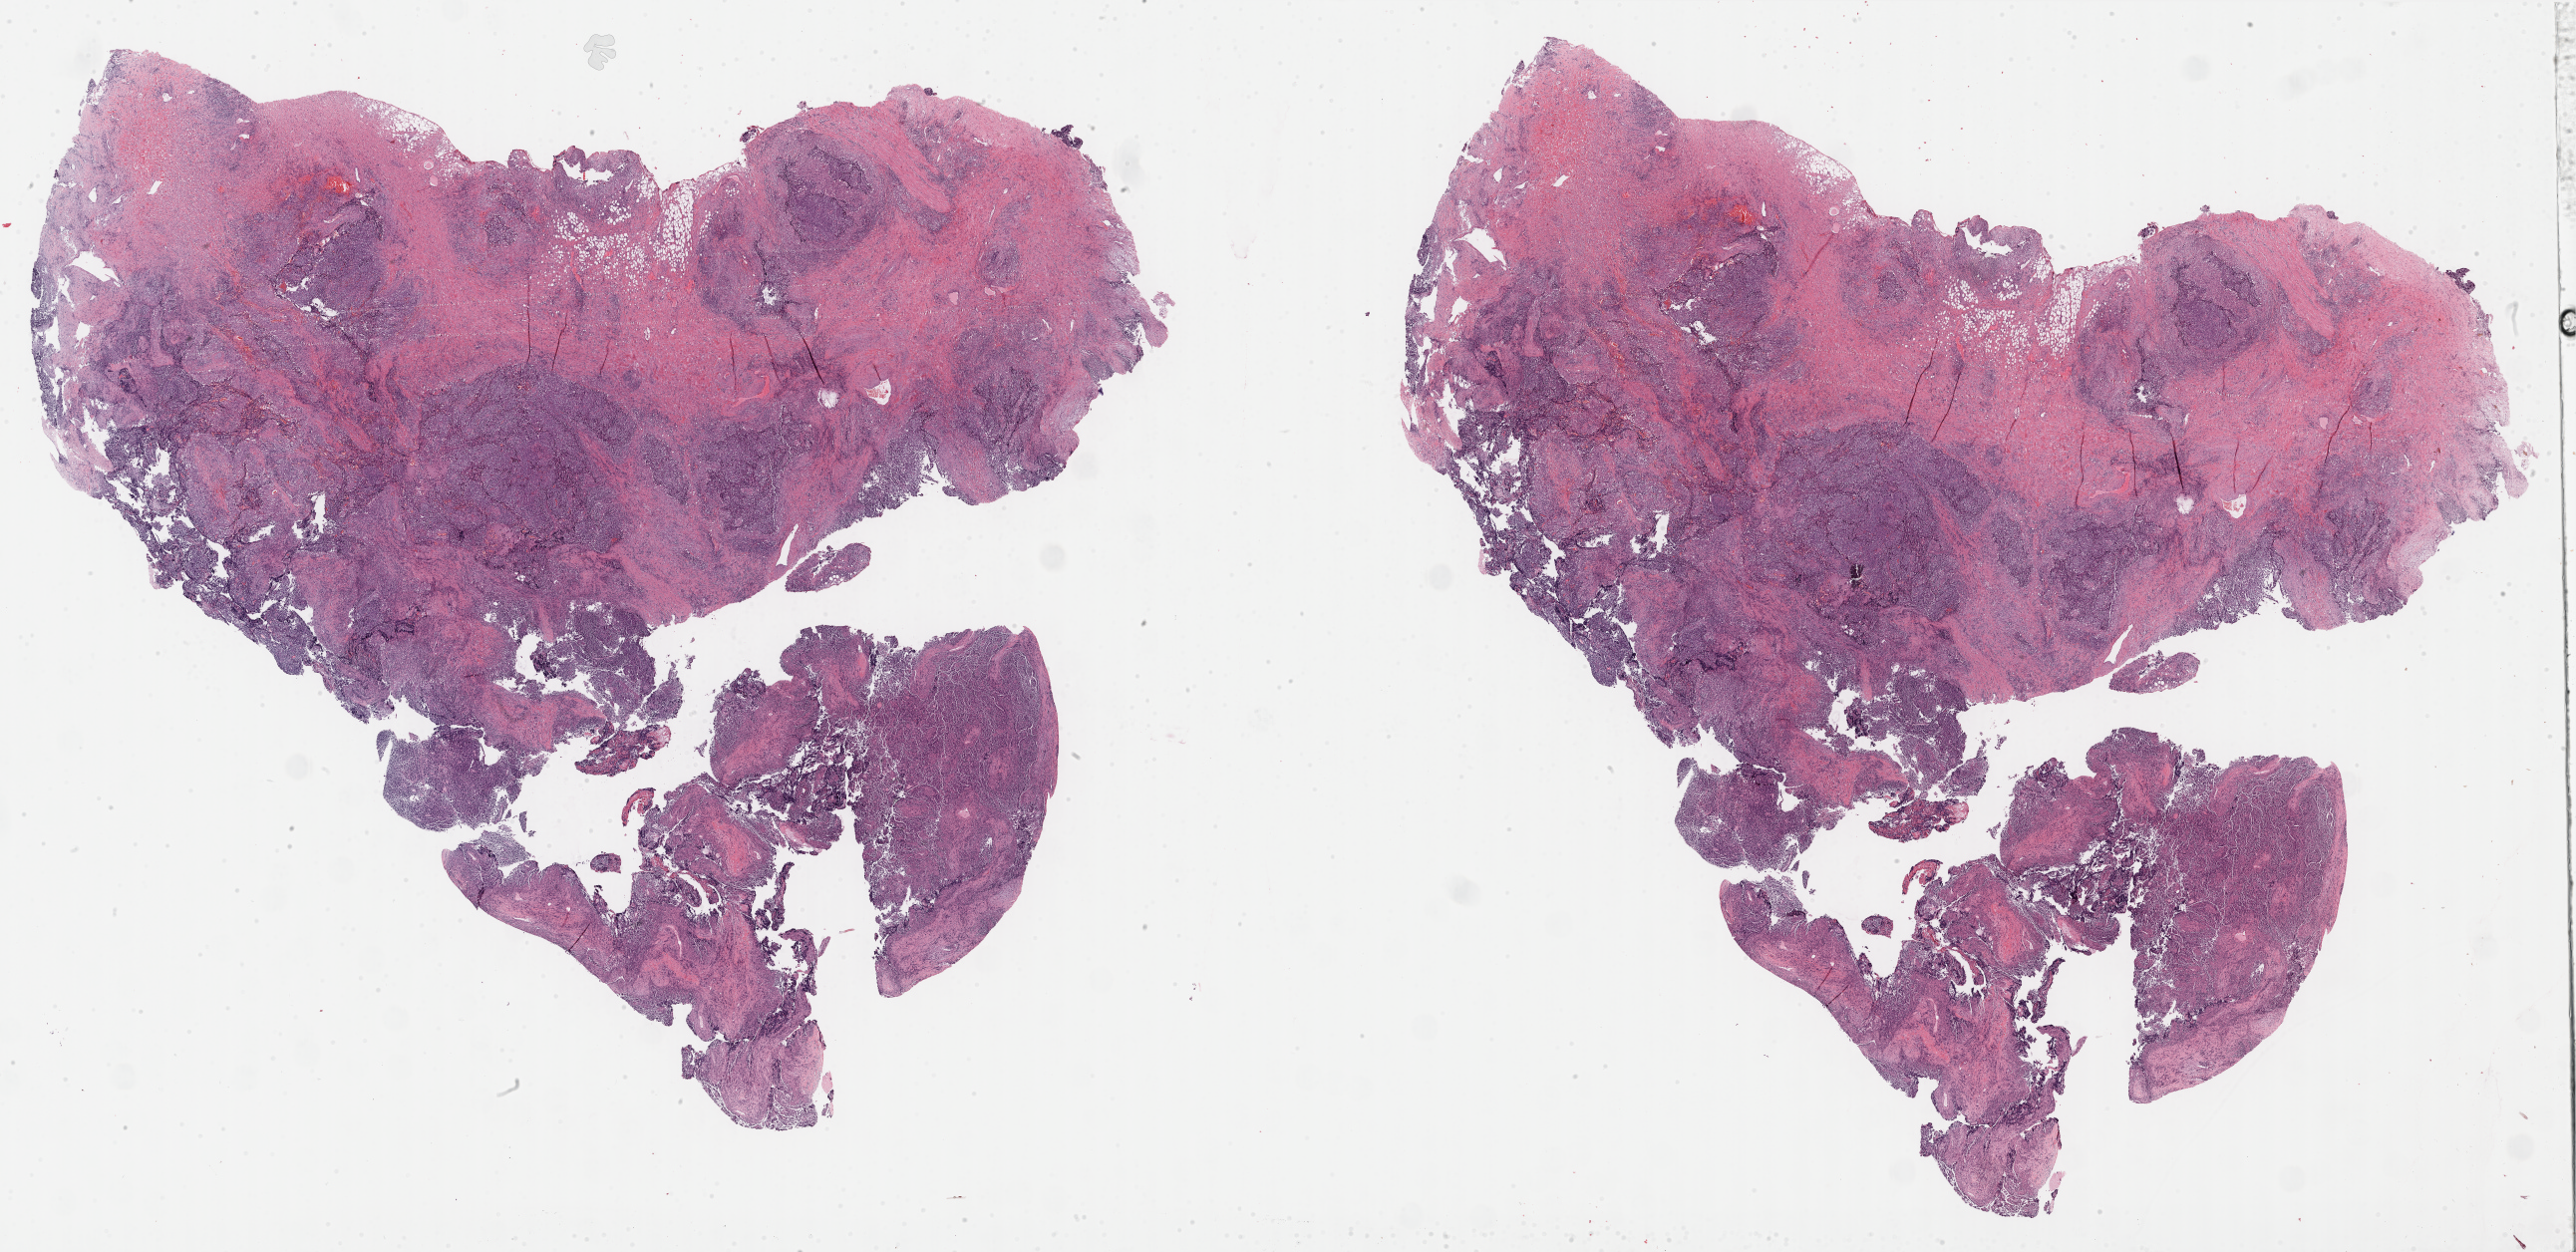
H&E whole-slide image — a low-resolution overview of the entire scanned area, about 41.7 x 20.3 mm, formalin-fixed paraffin-embedded (FFPE) diagnostic section, primary tumour sample from the ovary. Patient: female, age at initial diagnosis 81 years. Histologic grade: G3 (poorly differentiated).
FIGO stage: IIIC. Diagnosis: Serous cystadenocarcinoma, NOS.